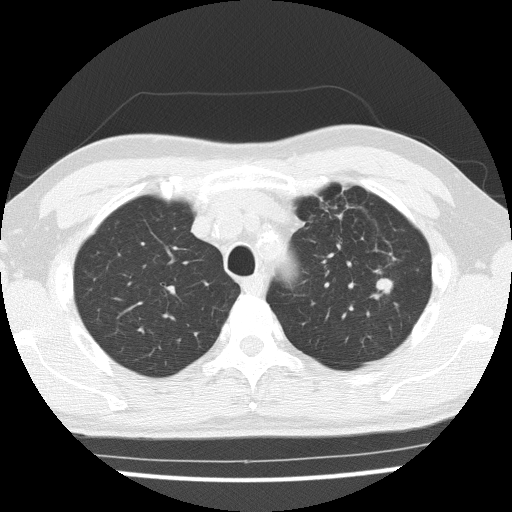
Low-dose screening chest CT, one axial slice; position 117 of 154 along the scan axis; reconstruction kernel FC51; 120 kVp; lung window (W 1500 / L -600 HU); 512 × 512 image matrix, field of view 330 × 330 mm.
Outlined on this slice (expert manual segmentation):
- lesion 1 (tumor, upper lobe of left lung): bounding box [x1, y1, x2, y2] px = [371, 279, 393, 299]